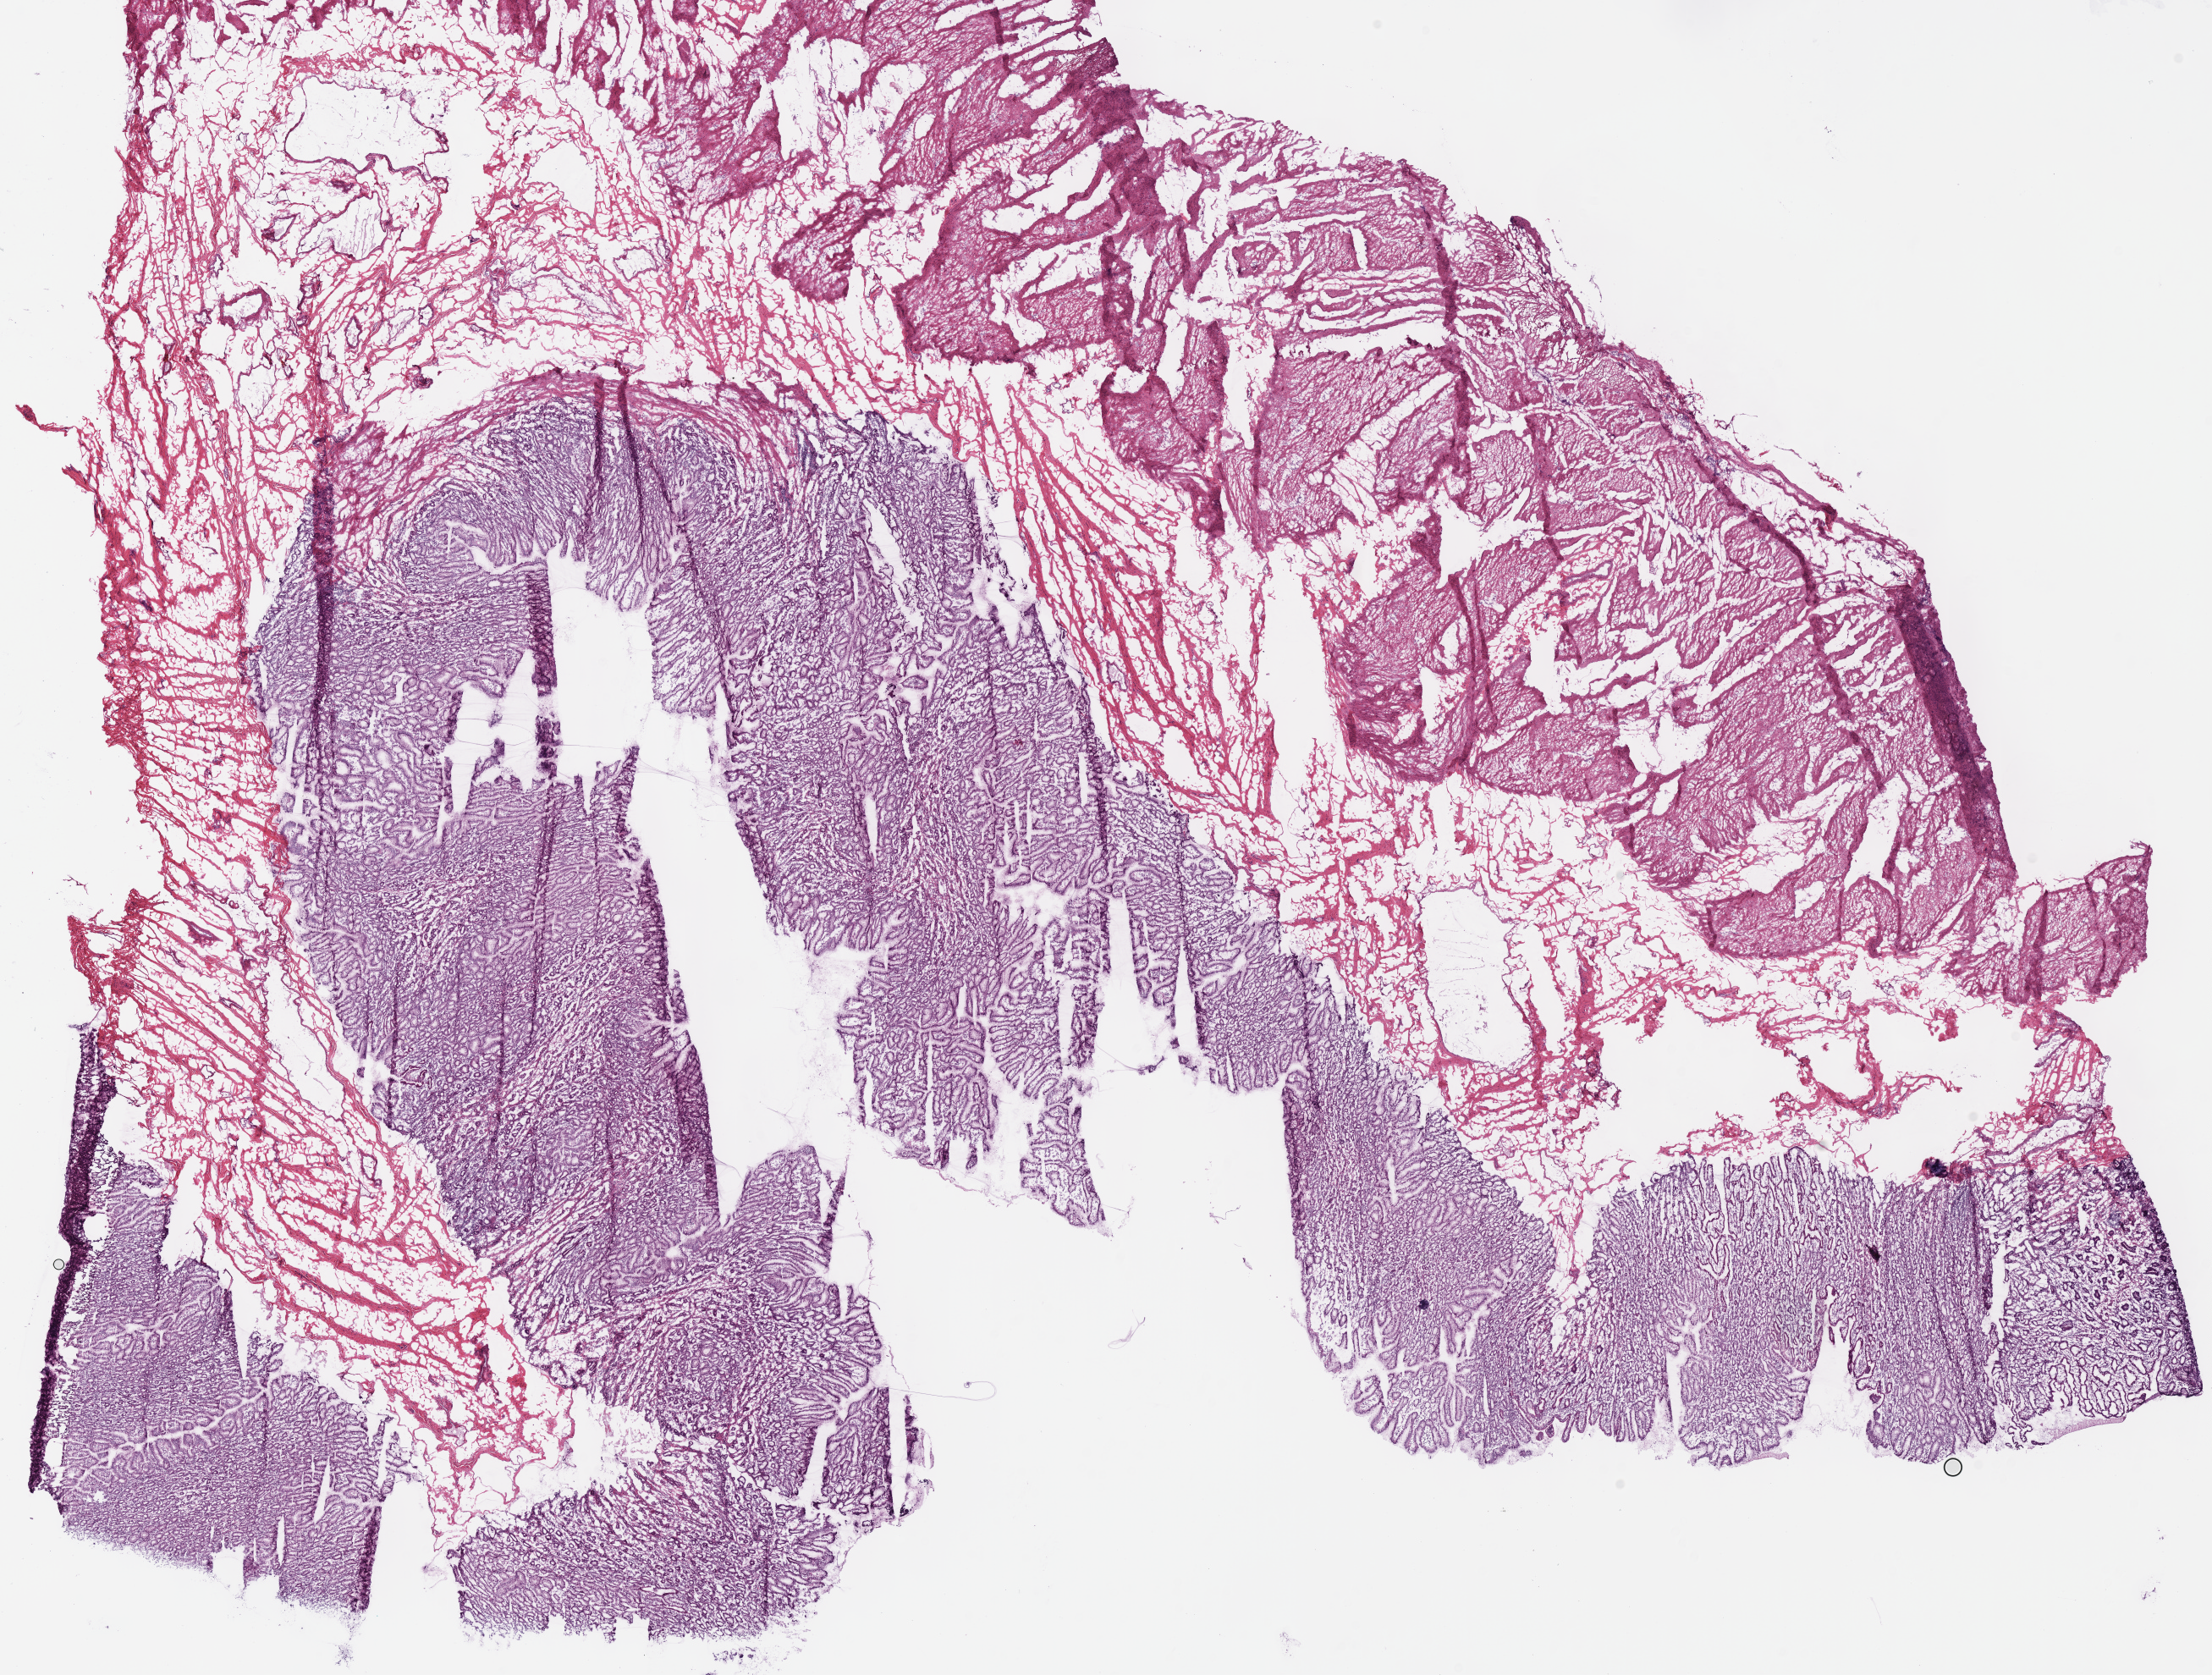
H&E whole-slide image — low-resolution overview of the scanned area, about 20.6 x 15.6 mm (from a 40x scan), frozen section, stomach, solid tissue normal (non-tumour tissue) sample. Female, age 62 years at initial diagnosis.
This section: solid tissue normal (non-tumour) sample from the same patient. Patient diagnosis: Adenocarcinoma, NOS (body of stomach).